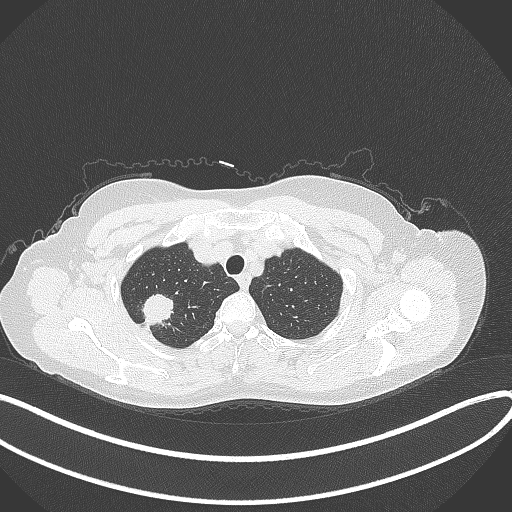
Chest CT, one axial slice; position 313 of 337 along the scan axis; 120 kVp; lung window (W 1500 / L -600 HU); 512 × 512 image matrix. Female patient, age 50 years. From the clinical record (not read from this slice): clinical TNM (as recorded): T1c N0 M0; histopathological grade: G2-3.
Annotated regions visible in this slice (rectangle marked by the reading radiologist):
- lung tumour (recorded histology: adenocarcinoma): bounding box (x1, y1, x2, y2) in pixels: (140, 290, 175, 325)